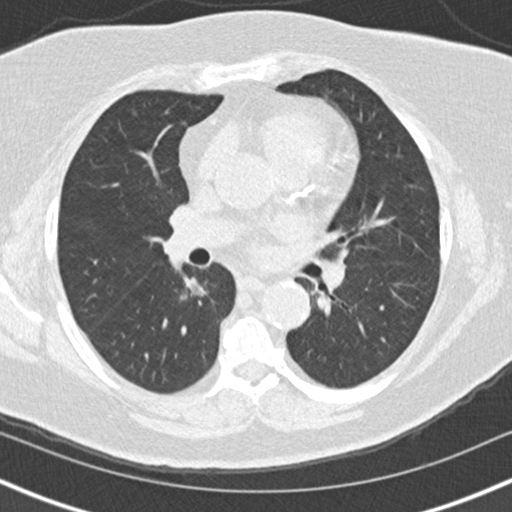
Low-dose screening chest CT, one axial slice; position 87 of 152 along the scan axis; 120 kVp; lung window (W 1500 / L -600 HU); 512 × 512 image matrix.
Annotated regions visible in this slice (manually delineated by an expert):
- lesion 1 (tumor, lower lobe of right lung): bounding box [x1, y1, x2, y2] px = [180, 275, 207, 300]